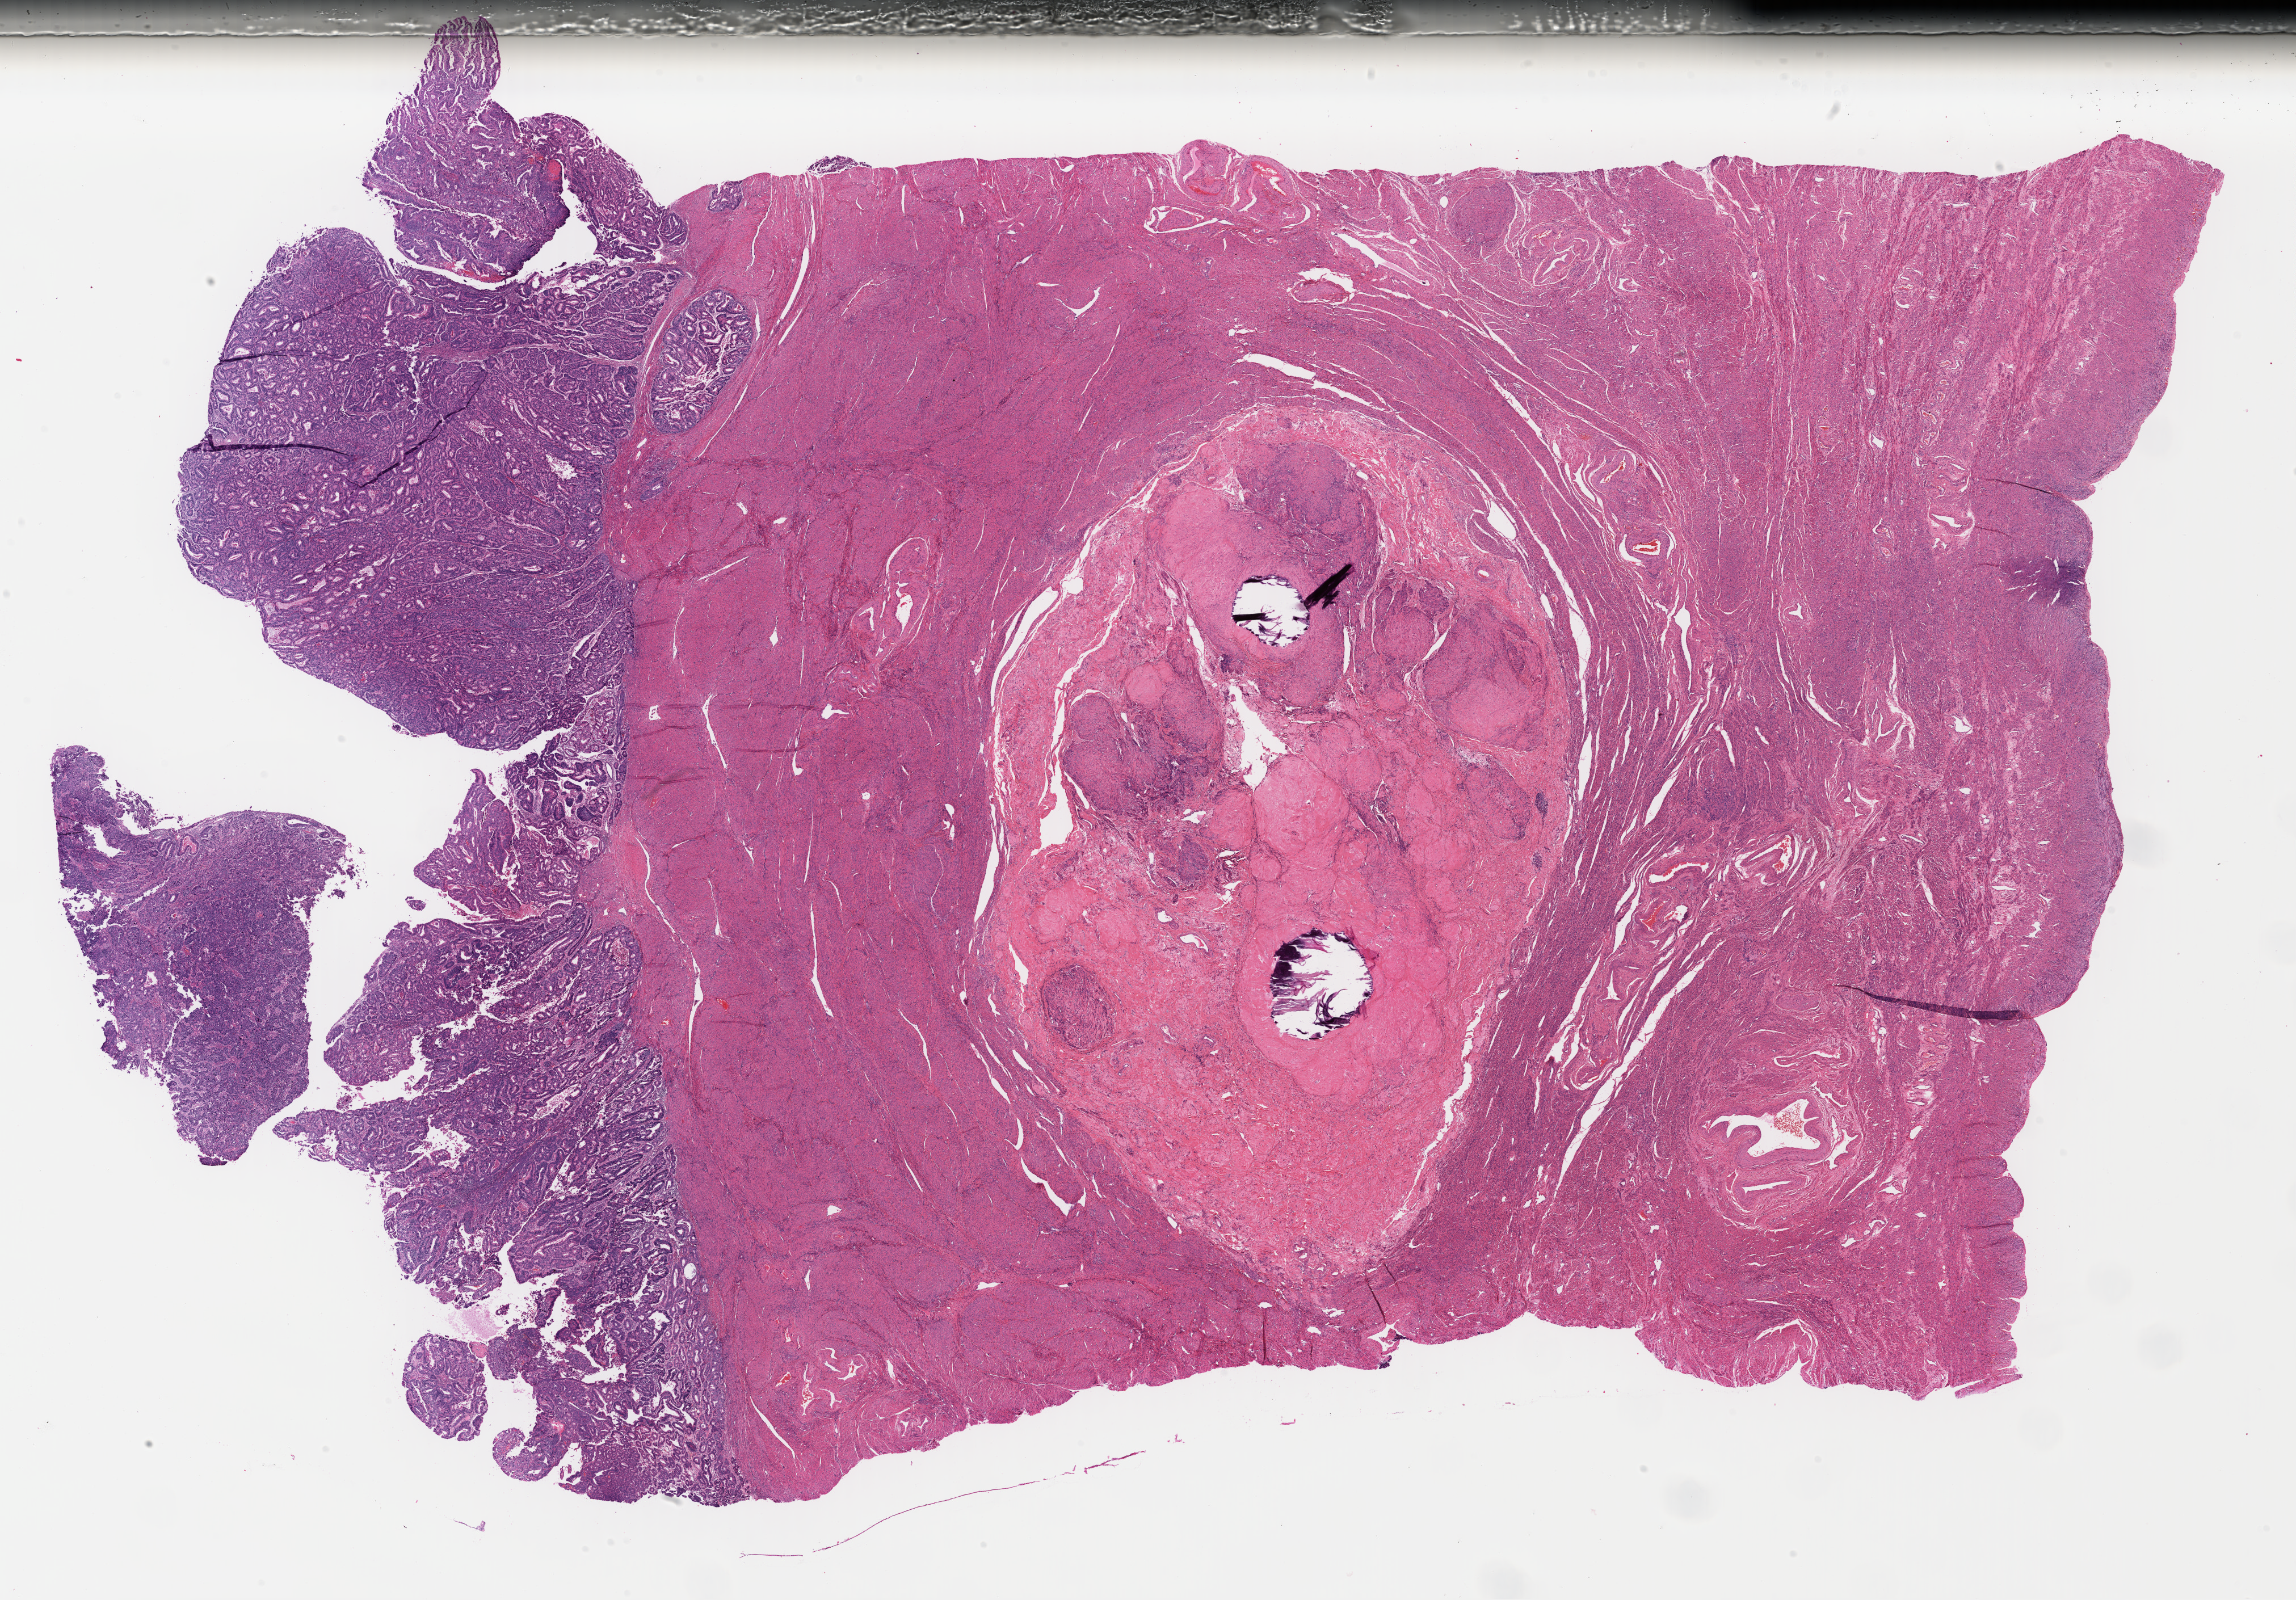
Whole-slide histology image, H&E-stained — shown as a low-resolution overview of the whole scanned area (about 31.8 x 22.2 mm), formalin-fixed paraffin-embedded (FFPE) diagnostic section, primary tumour sample from the uterus. Female, age 70 years at initial diagnosis. Histologic grade: G3 (poorly differentiated).
Histologic diagnosis: Endometrioid adenocarcinoma, NOS (endometrium). FIGO stage: IA.